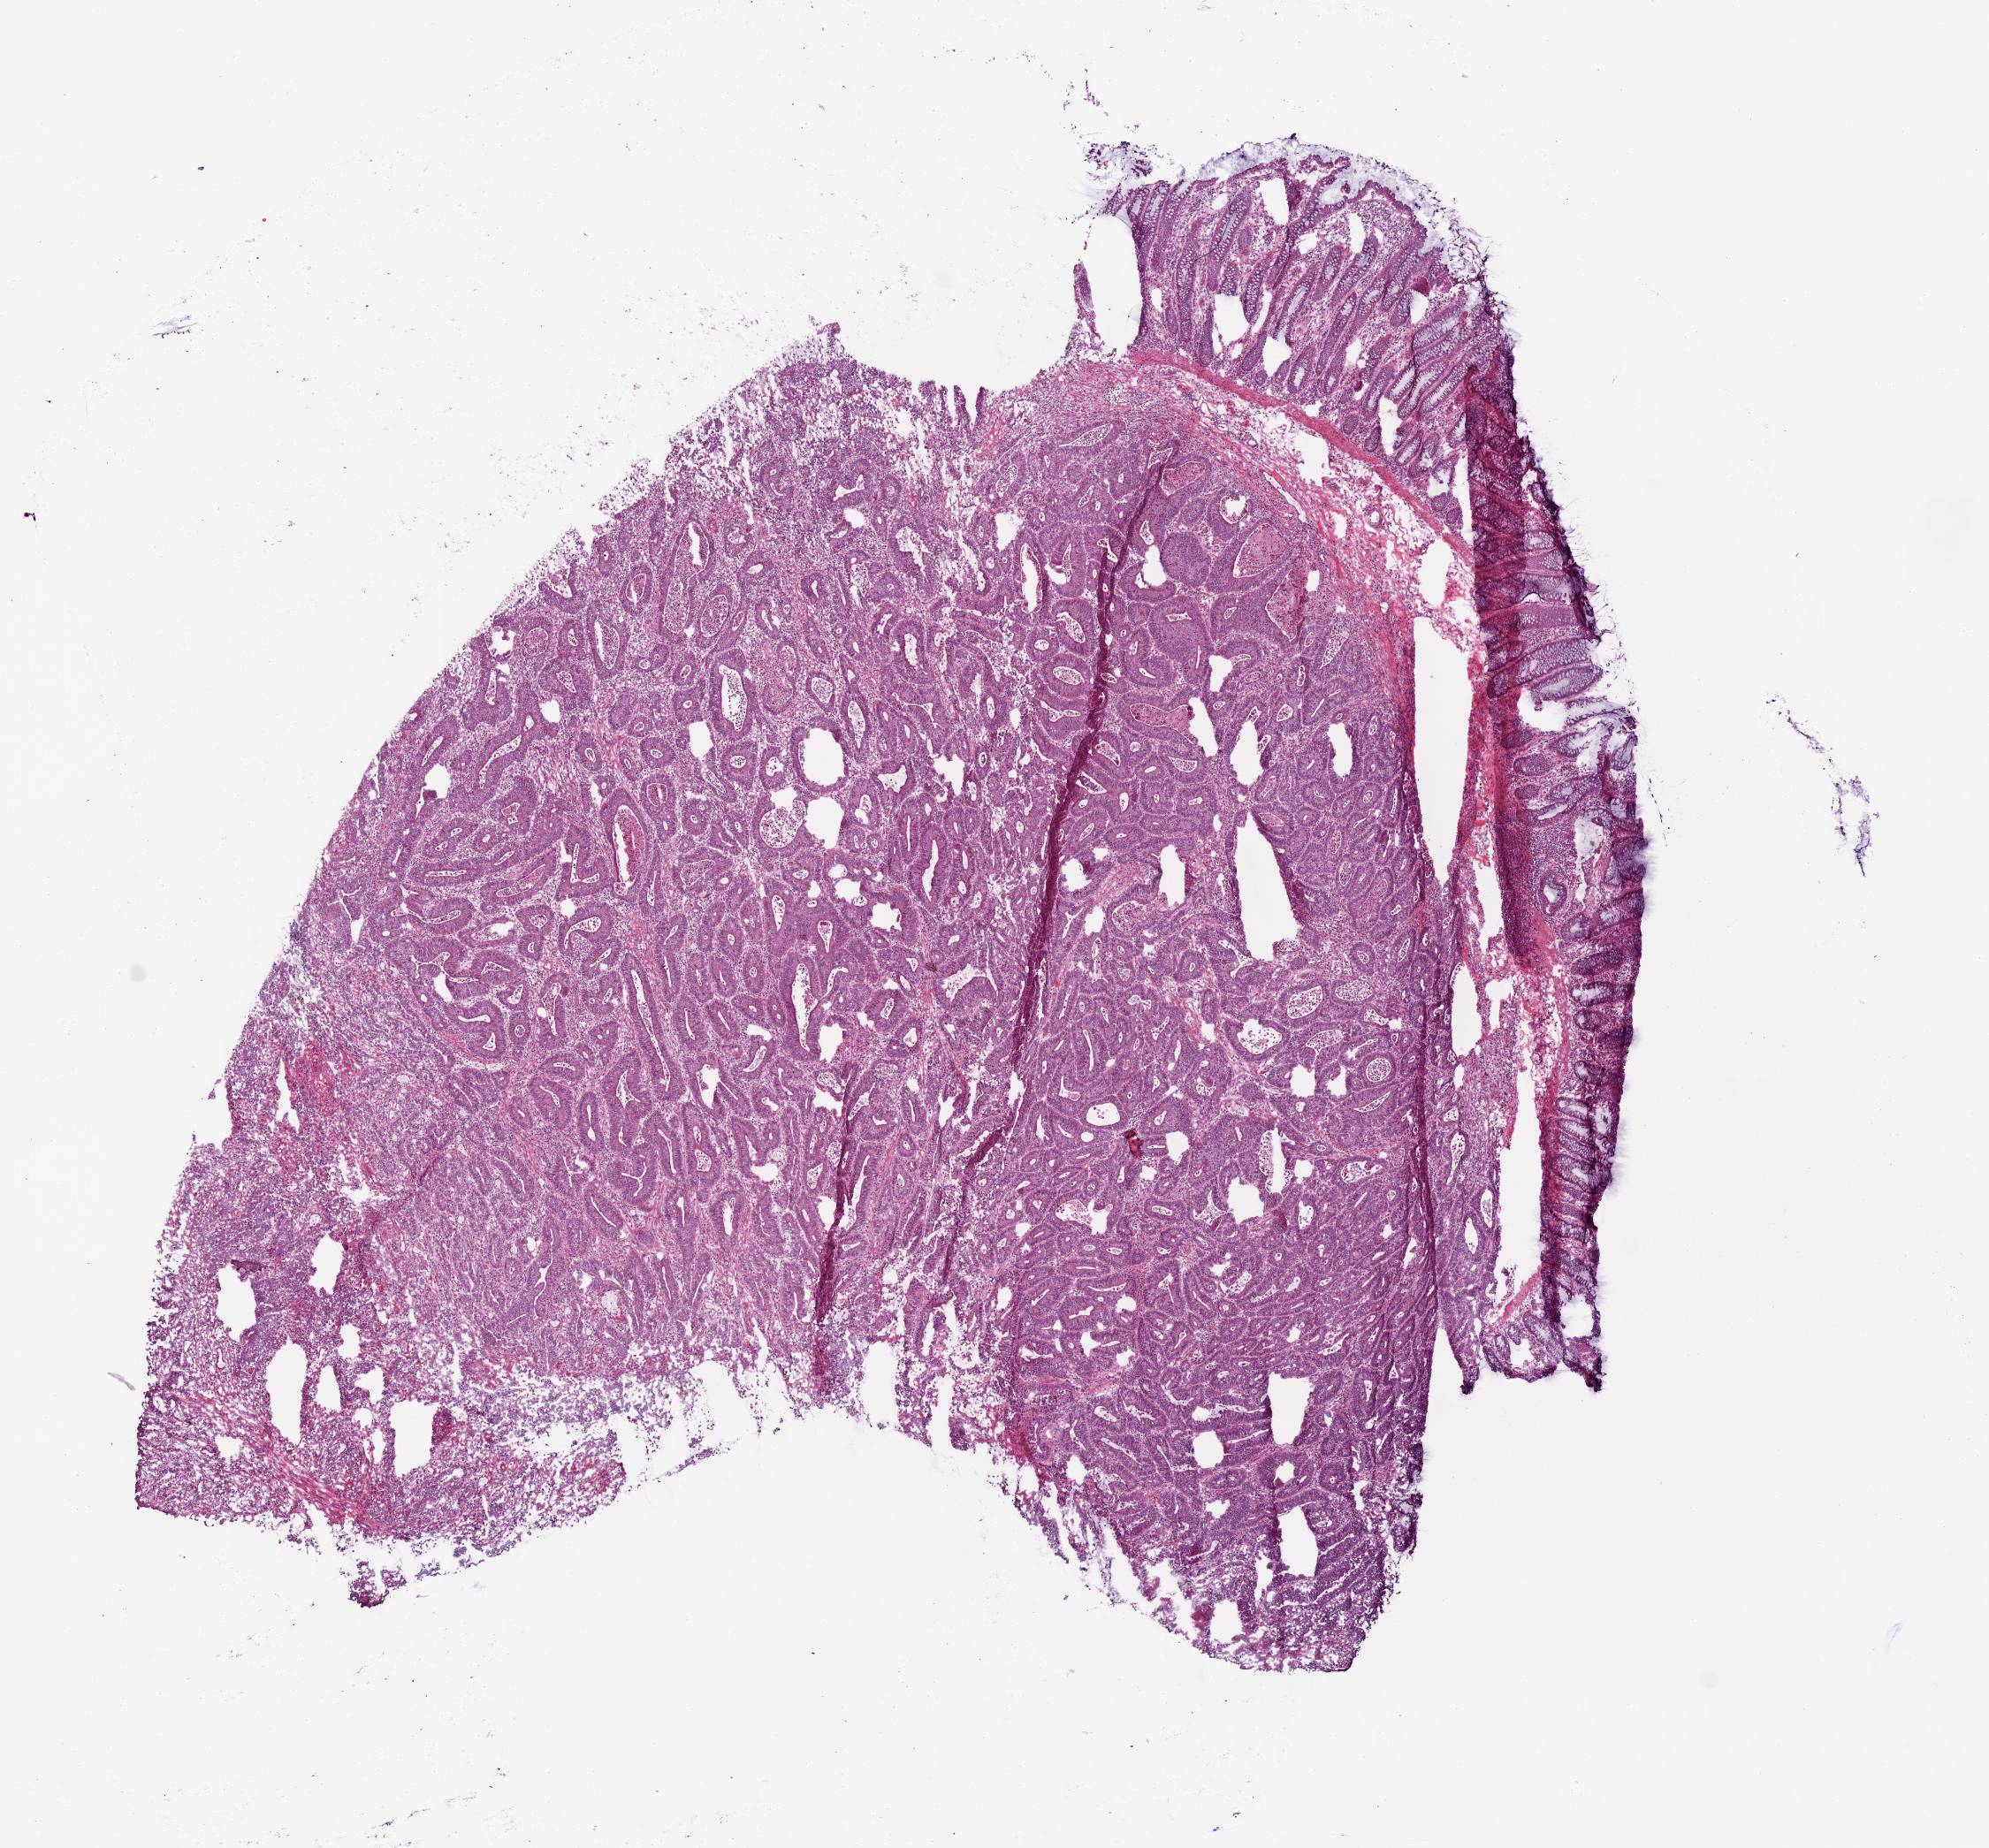
Digitized H&E-stained tissue section (whole slide), low-resolution overview of the scanned area, about 9.0 x 8.4 mm; frozen section from the bottom of the tissue portion; colon, primary tumour sample. Patient: male, age at initial diagnosis 82 years. Slide review estimates, as recorded: tumour cells 80%, tumour nuclei 85%, normal cells 5%, stromal cells 10%, necrosis 5%.
Diagnosis: Adenocarcinoma, NOS (ascending colon). AJCC pathologic stage: IIA (6th edition). Lymph nodes positive (case pathology): 0 of 16 examined.